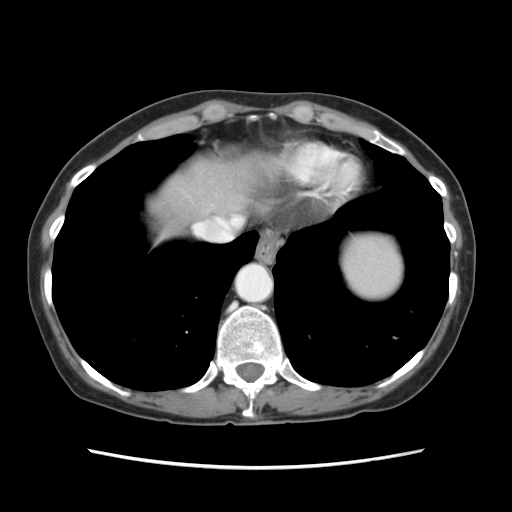
Contrast-enhanced abdominal CT, one axial slice. 120 kVp. Intravenous contrast given. Soft-tissue window (W 400 / L 40 HU). 2.5 mm slice thickness. 512 × 512 image matrix, field of view 330 × 330 mm. Female patient, age 70 years. Case-level facts recorded for this patient, not image findings: diagnosis: colorectal cancer liver metastases, imaged before liver resection; multiple liver metastases: no; largest metastasis: 2.5 cm.
Structures marked on this image (manually delineated by an expert):
- hepatic veins: bounding box <206,224,225,242> (left, top, right, bottom; pixels)
- liver: <145,159,259,233>
- planned liver remnant (the part of the liver to remain after resection): <160,159,266,223>